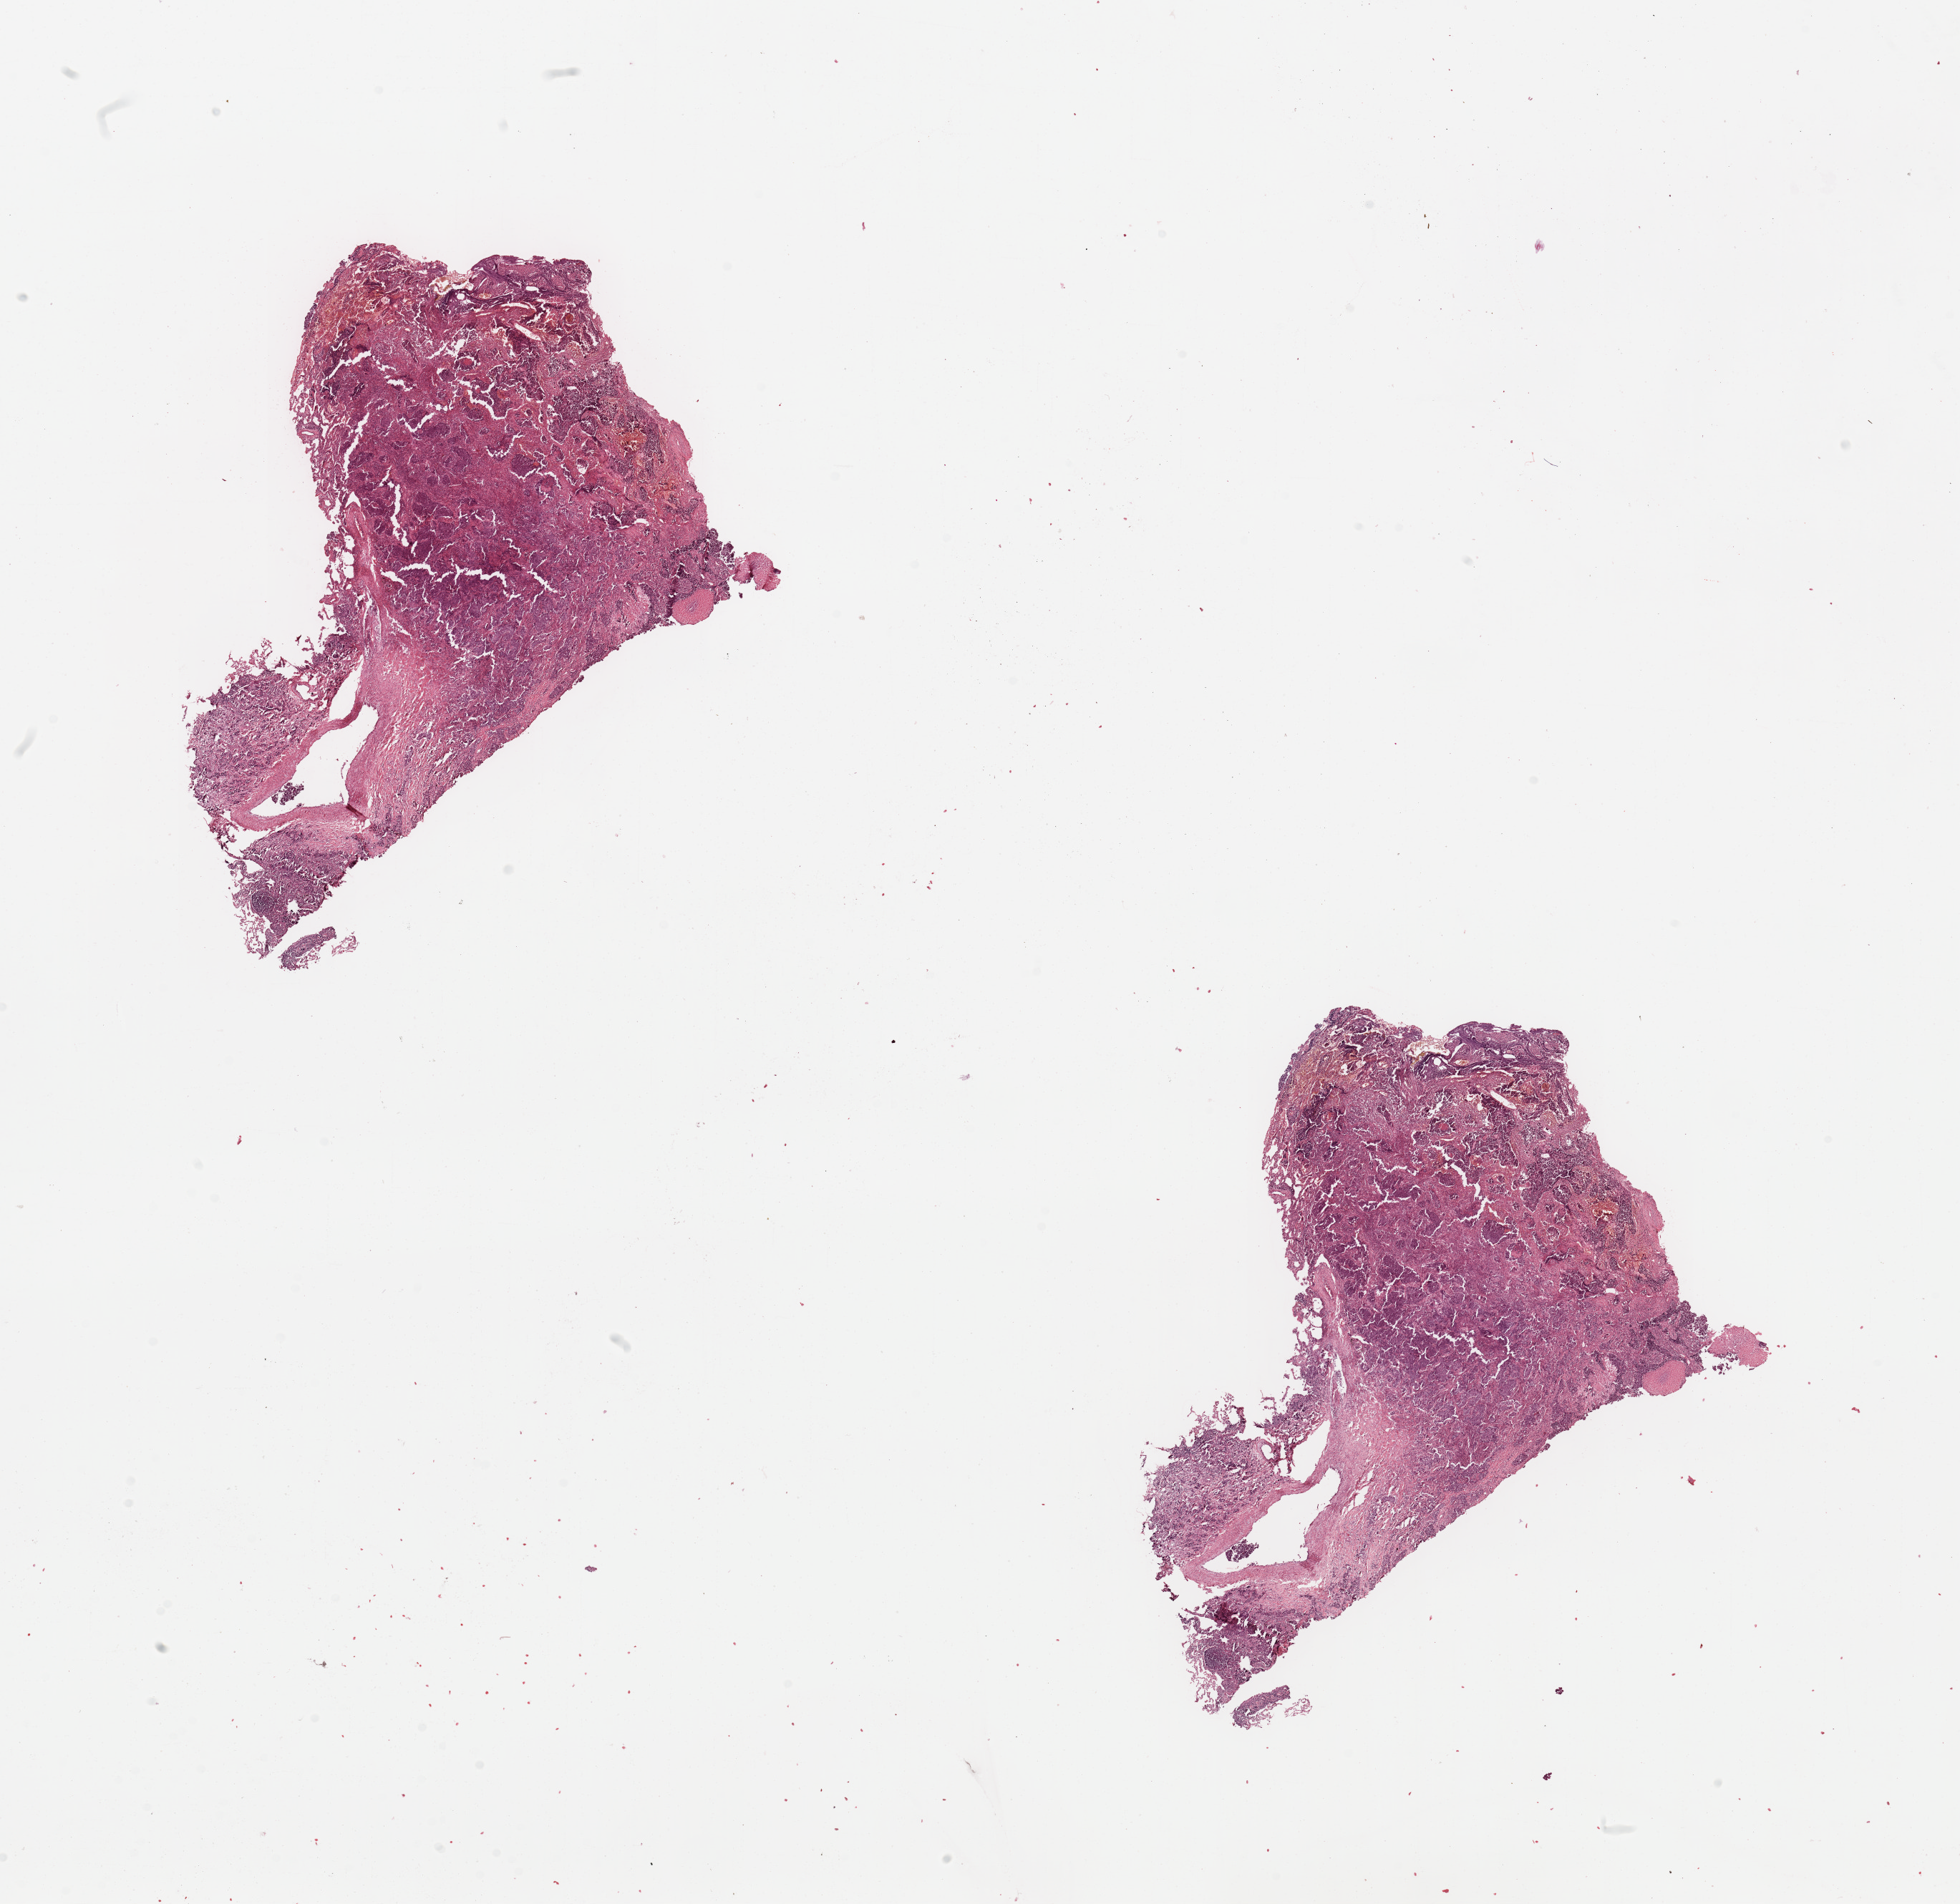
H&E whole-slide image, a low-resolution overview of the entire scanned area, about 21.7 x 21.0 mm; lung, tumour tissue. 54-year-old male patient. Histologic grade: G2 (moderately differentiated).
Primary tumour site (as recorded): left upper lobe. Diagnosis: Adenocarcinoma, NOS. AJCC pathologic stage: IA.